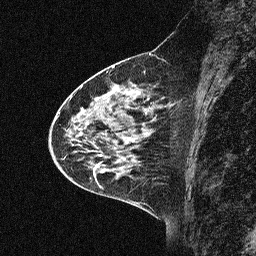
Breast MRI (dynamic contrast-enhanced), one sagittal slice; position 25 of 64 along the scan axis; dynamic contrast-enhanced study with each time point stored as its own series, time point 2 of 3 at this slice position (early post-contrast, ordered by acquisition time); 1.5 T; TE 4.5 ms, TR 11 ms; 2.06 mm slice thickness; 256 × 256 image matrix, field of view 200 × 200 mm. Female patient, age 46 years. Case-level facts recorded for this patient, not image findings: setting: breast cancer imaged before/during neoadjuvant chemotherapy; receptor status: HER2-positive.
Structures marked on this image (semi-automatically segmented with operator editing):
- analysis volume of interest (the breast-tissue region the enhancement analysis was run in; not a lesion): box from (x=46, y=51) to (x=180, y=169) px
- tumour enhancement mask (voxels above the 90 % enhancement threshold inside the analysis volume of interest): (x=87, y=99)–(x=109, y=167)